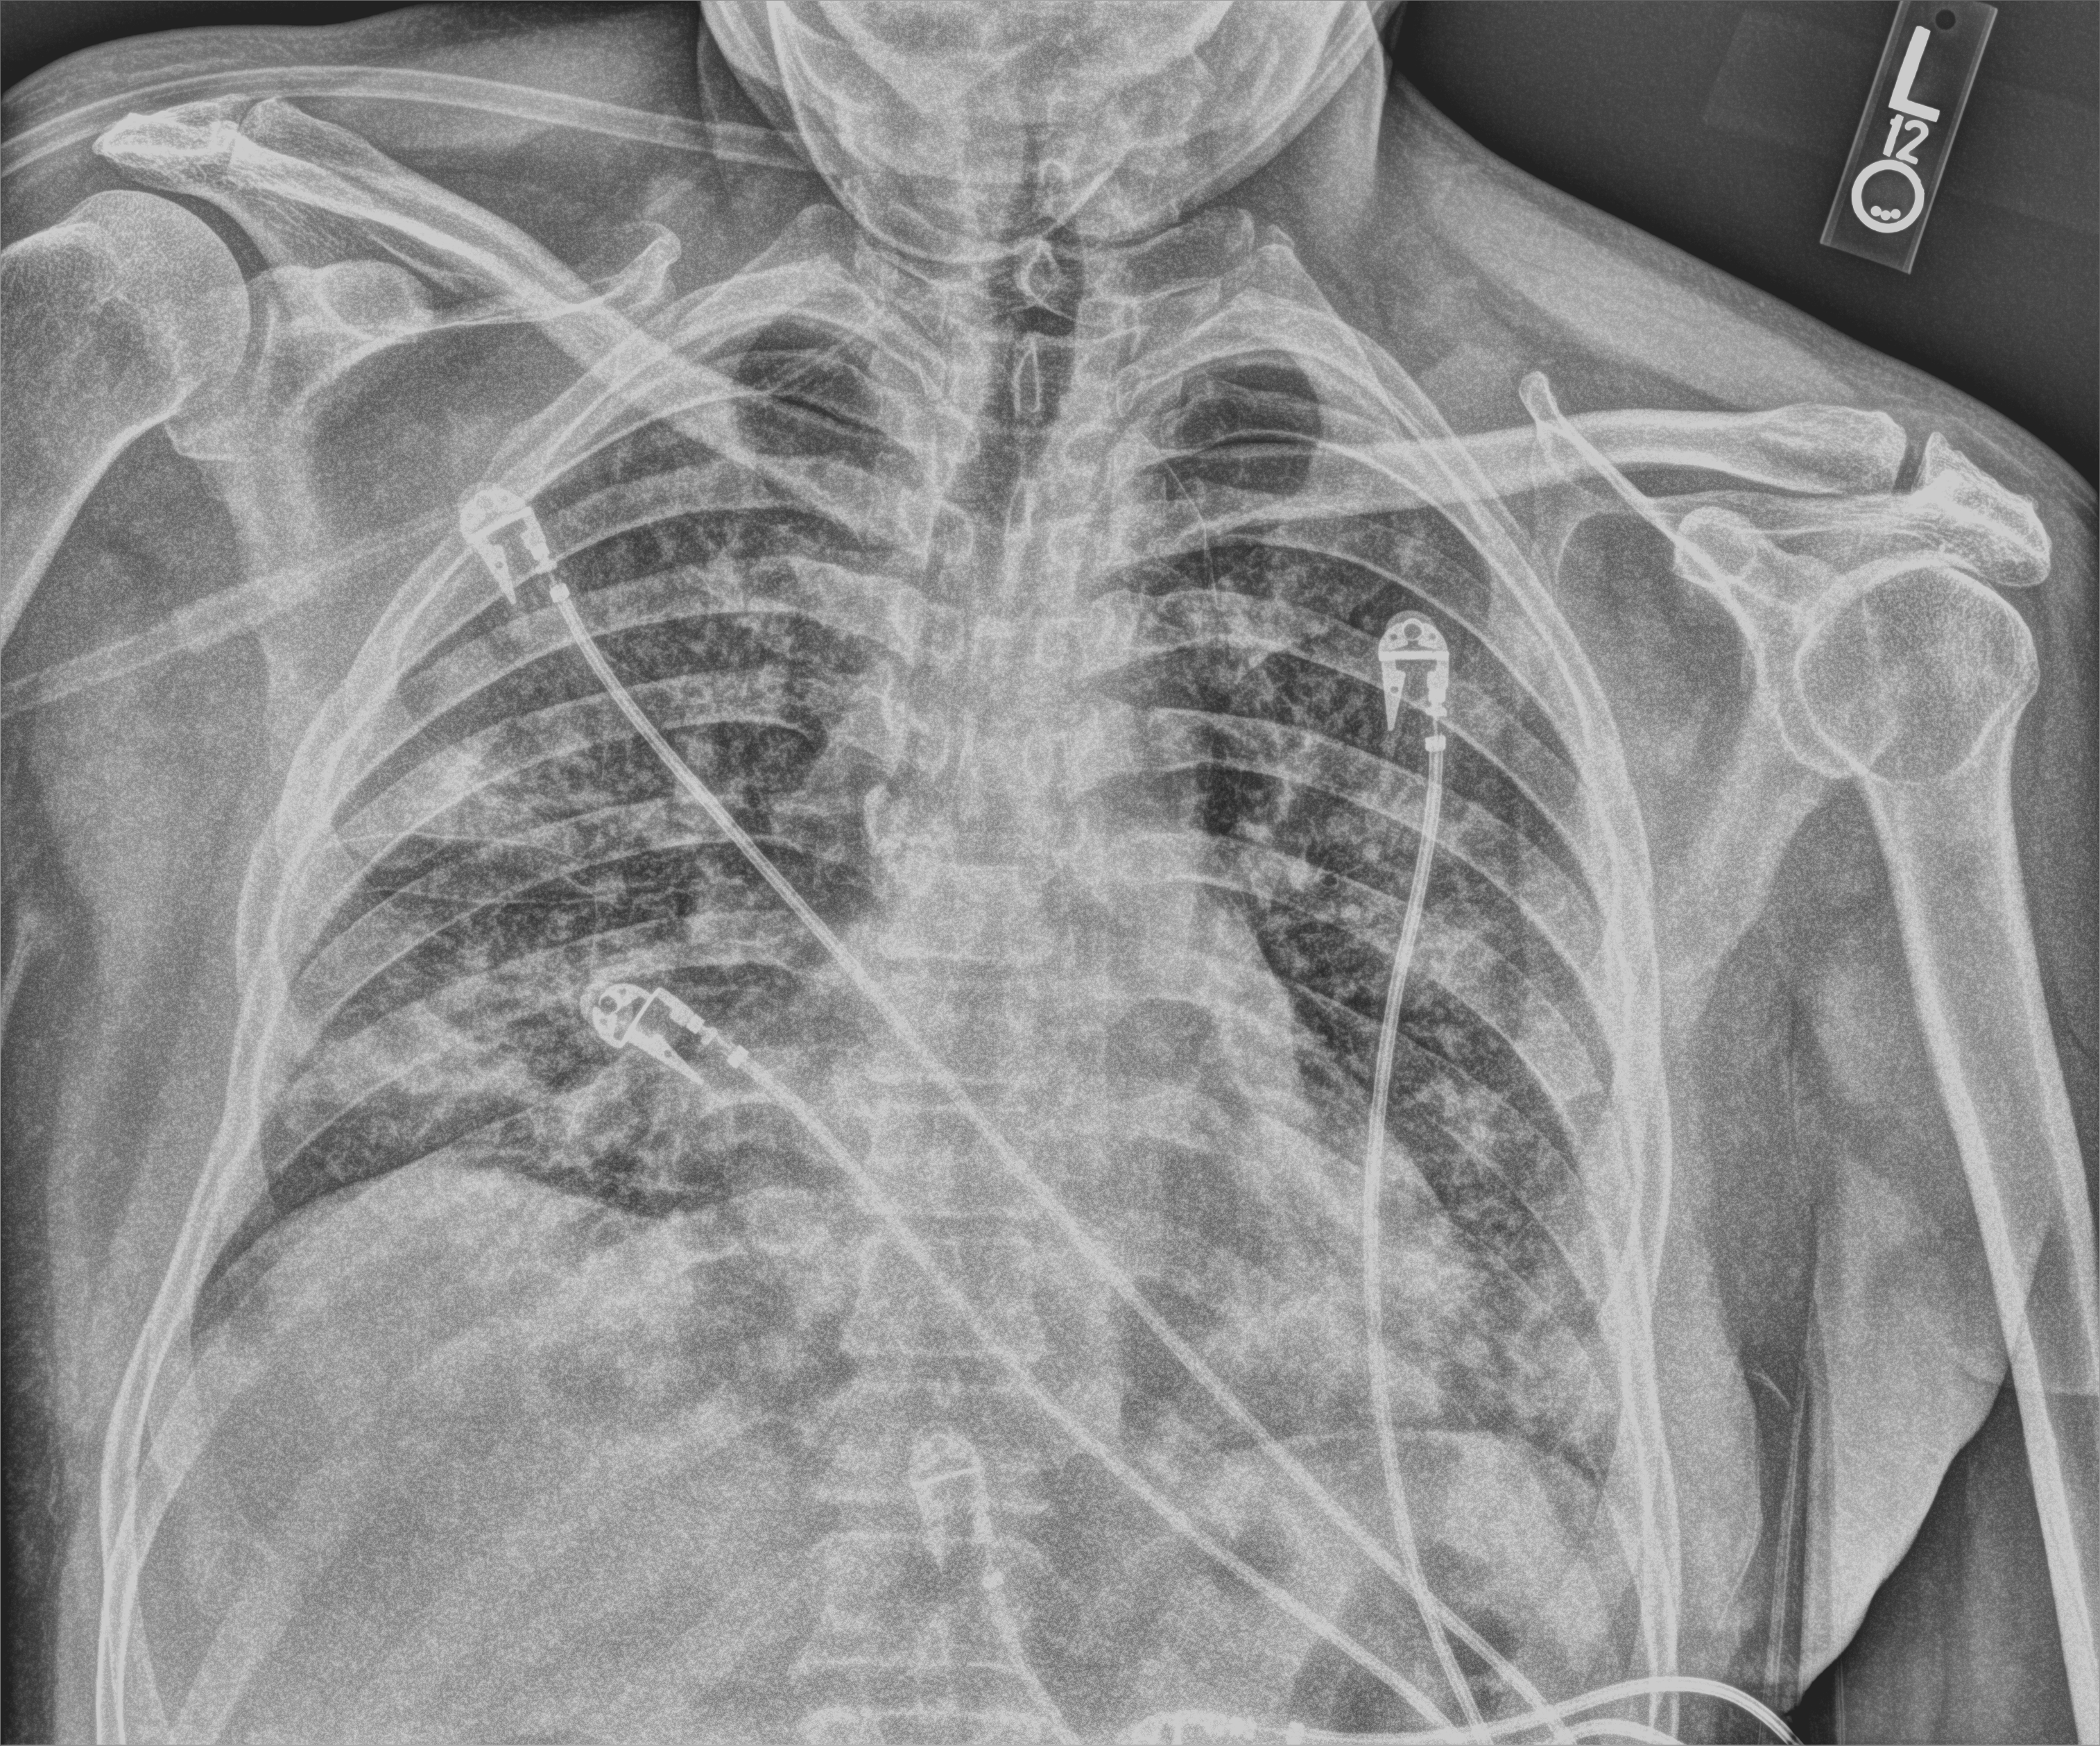
Chest X-ray (portable), anteroposterior (AP) projection. Patient hospitalised with COVID-19; male, aged 18–59 years.
From the hospital-stay record, not from the radiograph (when in the stay this image was taken is not recorded):
- other chronic lung disease (admission record): no
- smoking status (admission record): never
- mechanically ventilated during this hospital stay: no